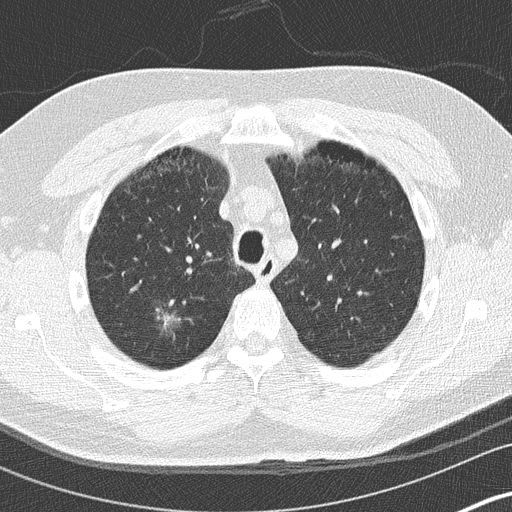
Low-dose screening chest CT, axial slice; baseline annual screen; lung window (W 1500 / L -600 HU); lung (sharp) reconstruction kernel (B50f); 512 × 512 image matrix, field of view 310 × 310 mm. Male participant, aged 59 years at enrolment. Current smoker at enrolment.
Lesion marked by an expert reader, box from (x=144, y=290) to (x=197, y=343) px. The exam's reader record, not a measurement of the box and not confirmed to be the same lesion: non-calcified nodule or mass ≥4 mm, right upper lobe, 16 × 16 mm, ground glass attenuation. Participant outcome: lung cancer diagnosed 456 days after this screen — bronchiolo-alveolar adenocarcinoma, NOS, right lower lobe, stage IA (AJCC 6th edition), 15 mm at pathology.